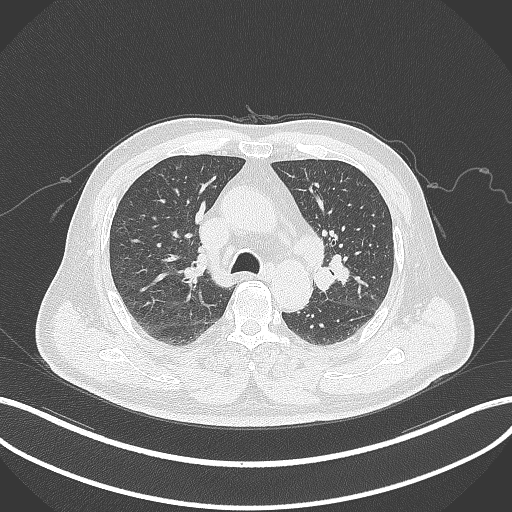
Chest CT, one axial slice; slice 200 of 286 in the series (ordered by position); lung window (W 1500 / L -600 HU); 512 × 512 image matrix, field of view 400 × 400 mm. Patient: male, 67 years. From the clinical record (not read from this slice): clinical TNM (as recorded): T2a N1 M0.
Annotated regions visible in this slice (bounding box drawn by a radiologist):
- lung tumour (recorded histology: adenocarcinoma): bounding box (x1, y1, x2, y2) in pixels: (311, 254, 348, 292)